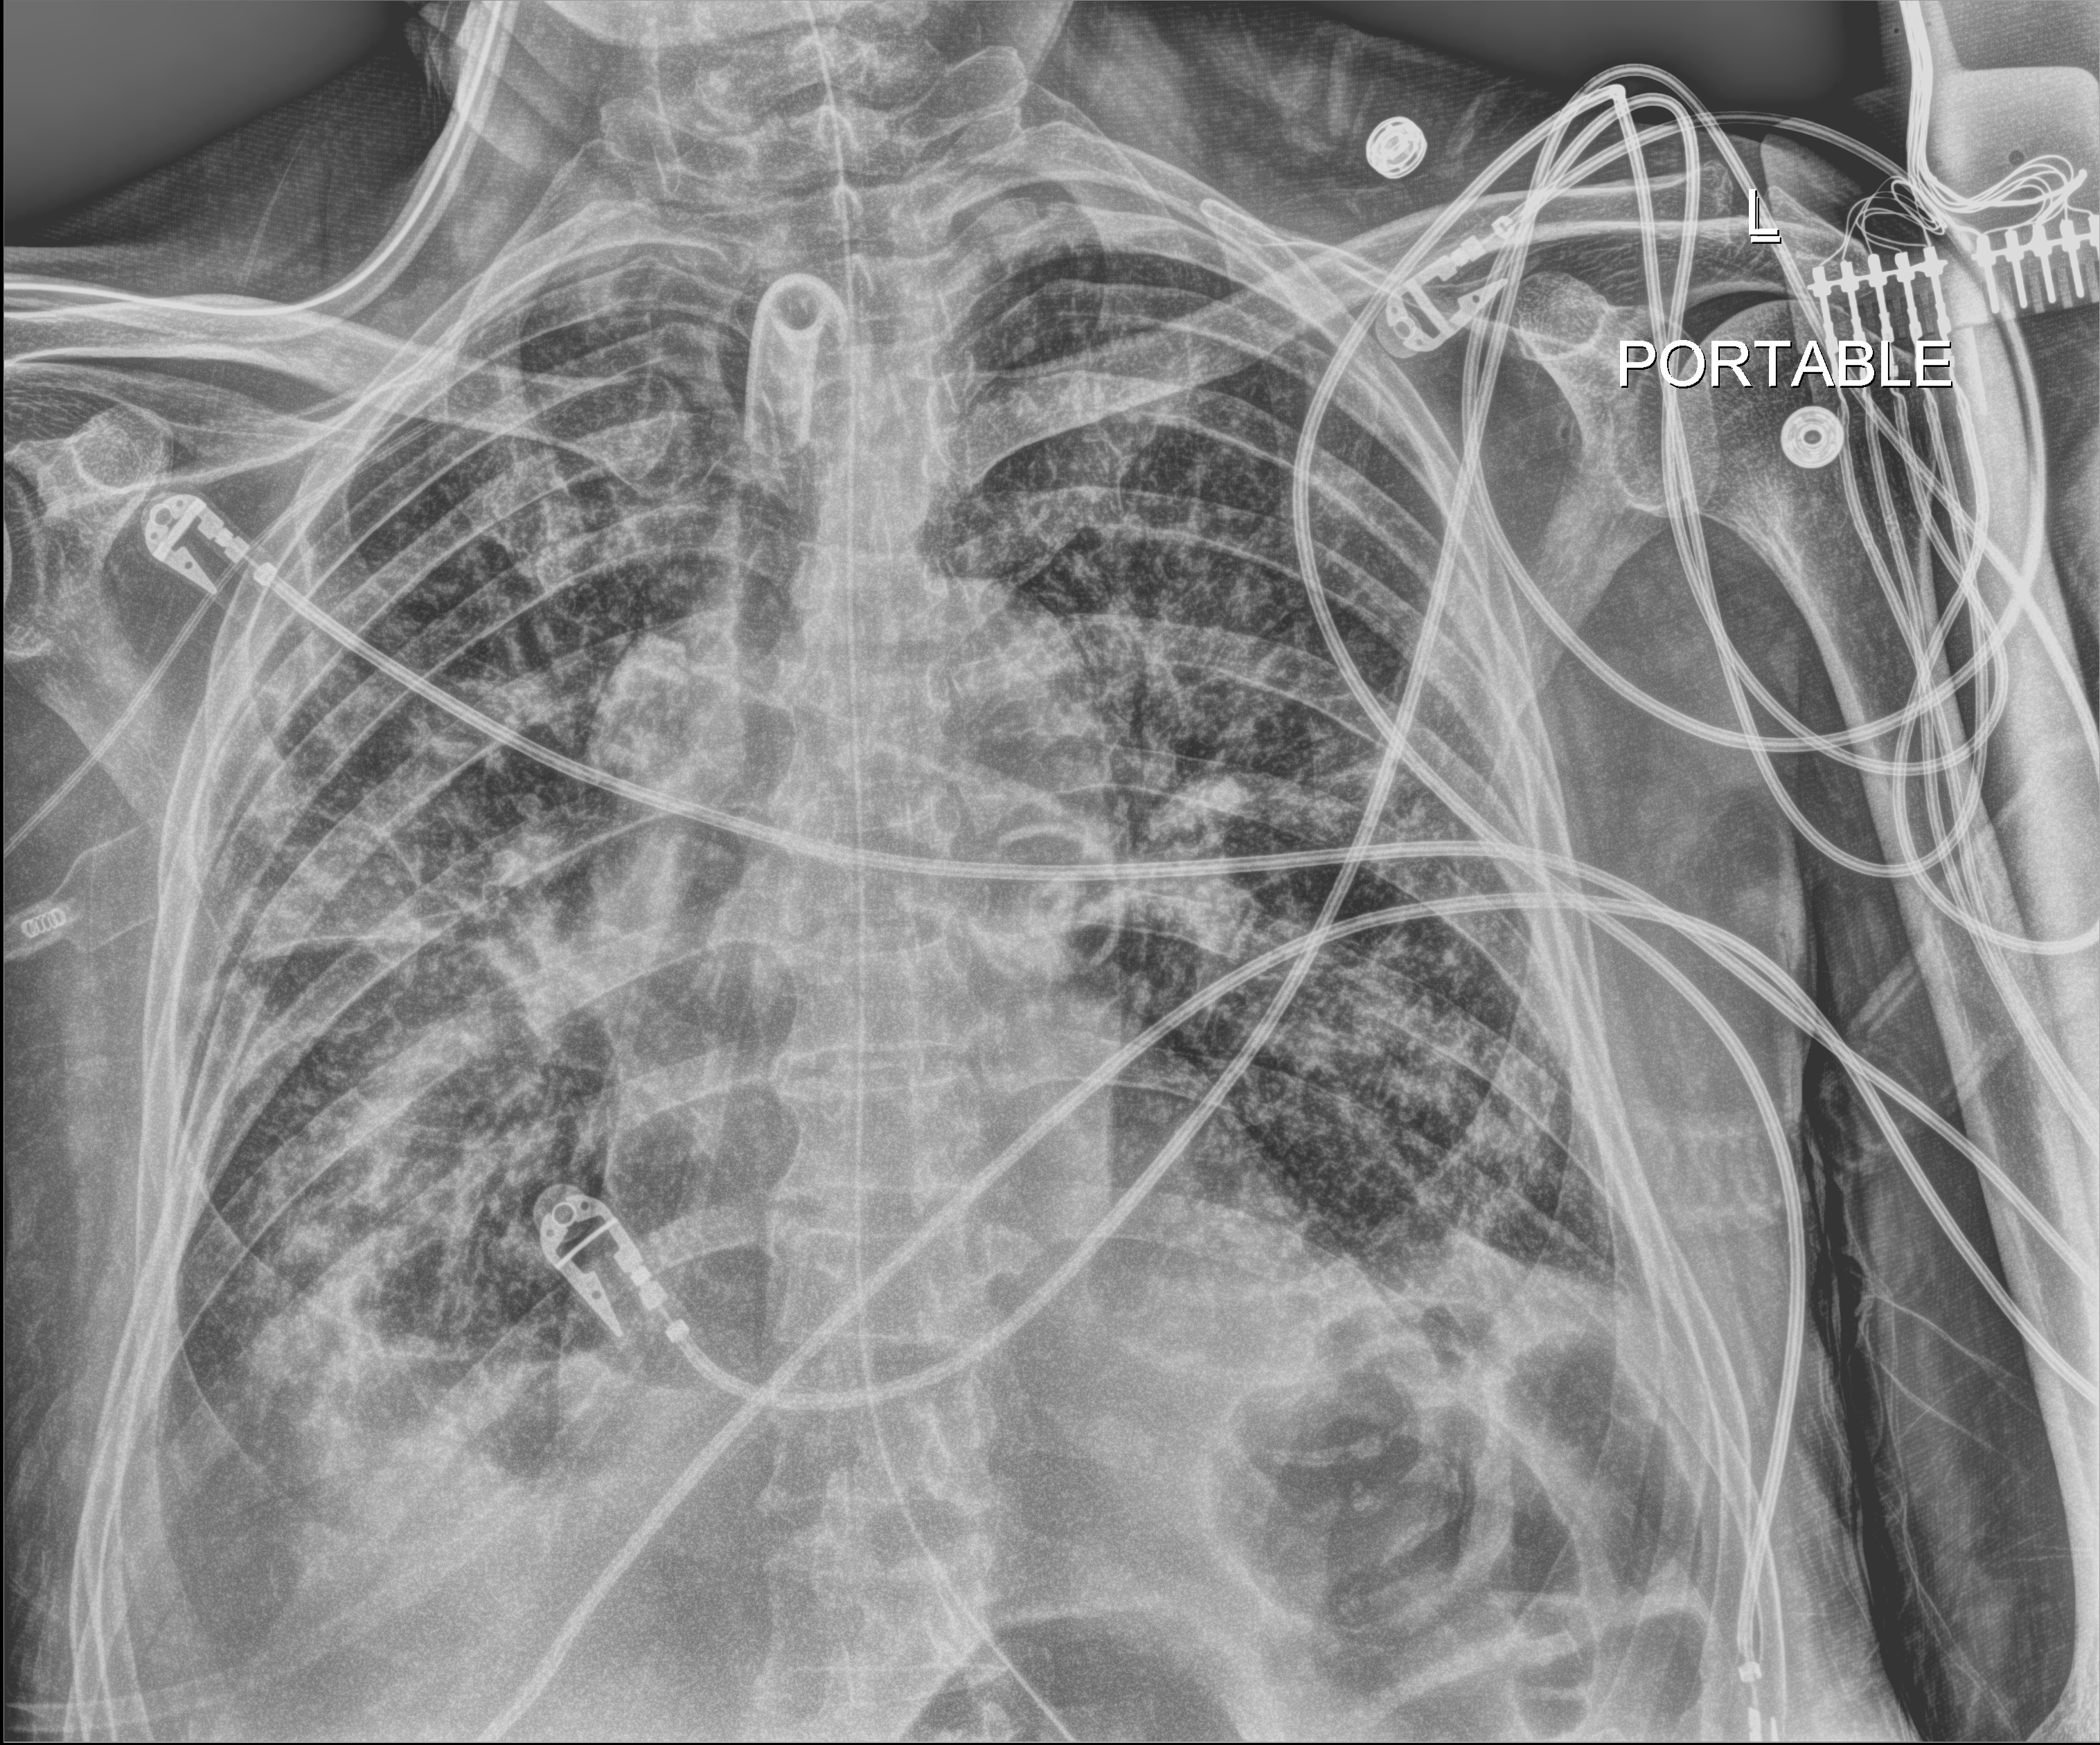
Bedside chest radiograph (digital radiography); anteroposterior (AP) projection. Male patient hospitalised with COVID-19, age 75–90 years.
From the hospital-stay record, not from the radiograph (when in the stay this image was taken is not recorded):
- admitted to intensive care during this hospital stay: yes
- mechanically ventilated during this hospital stay: yes